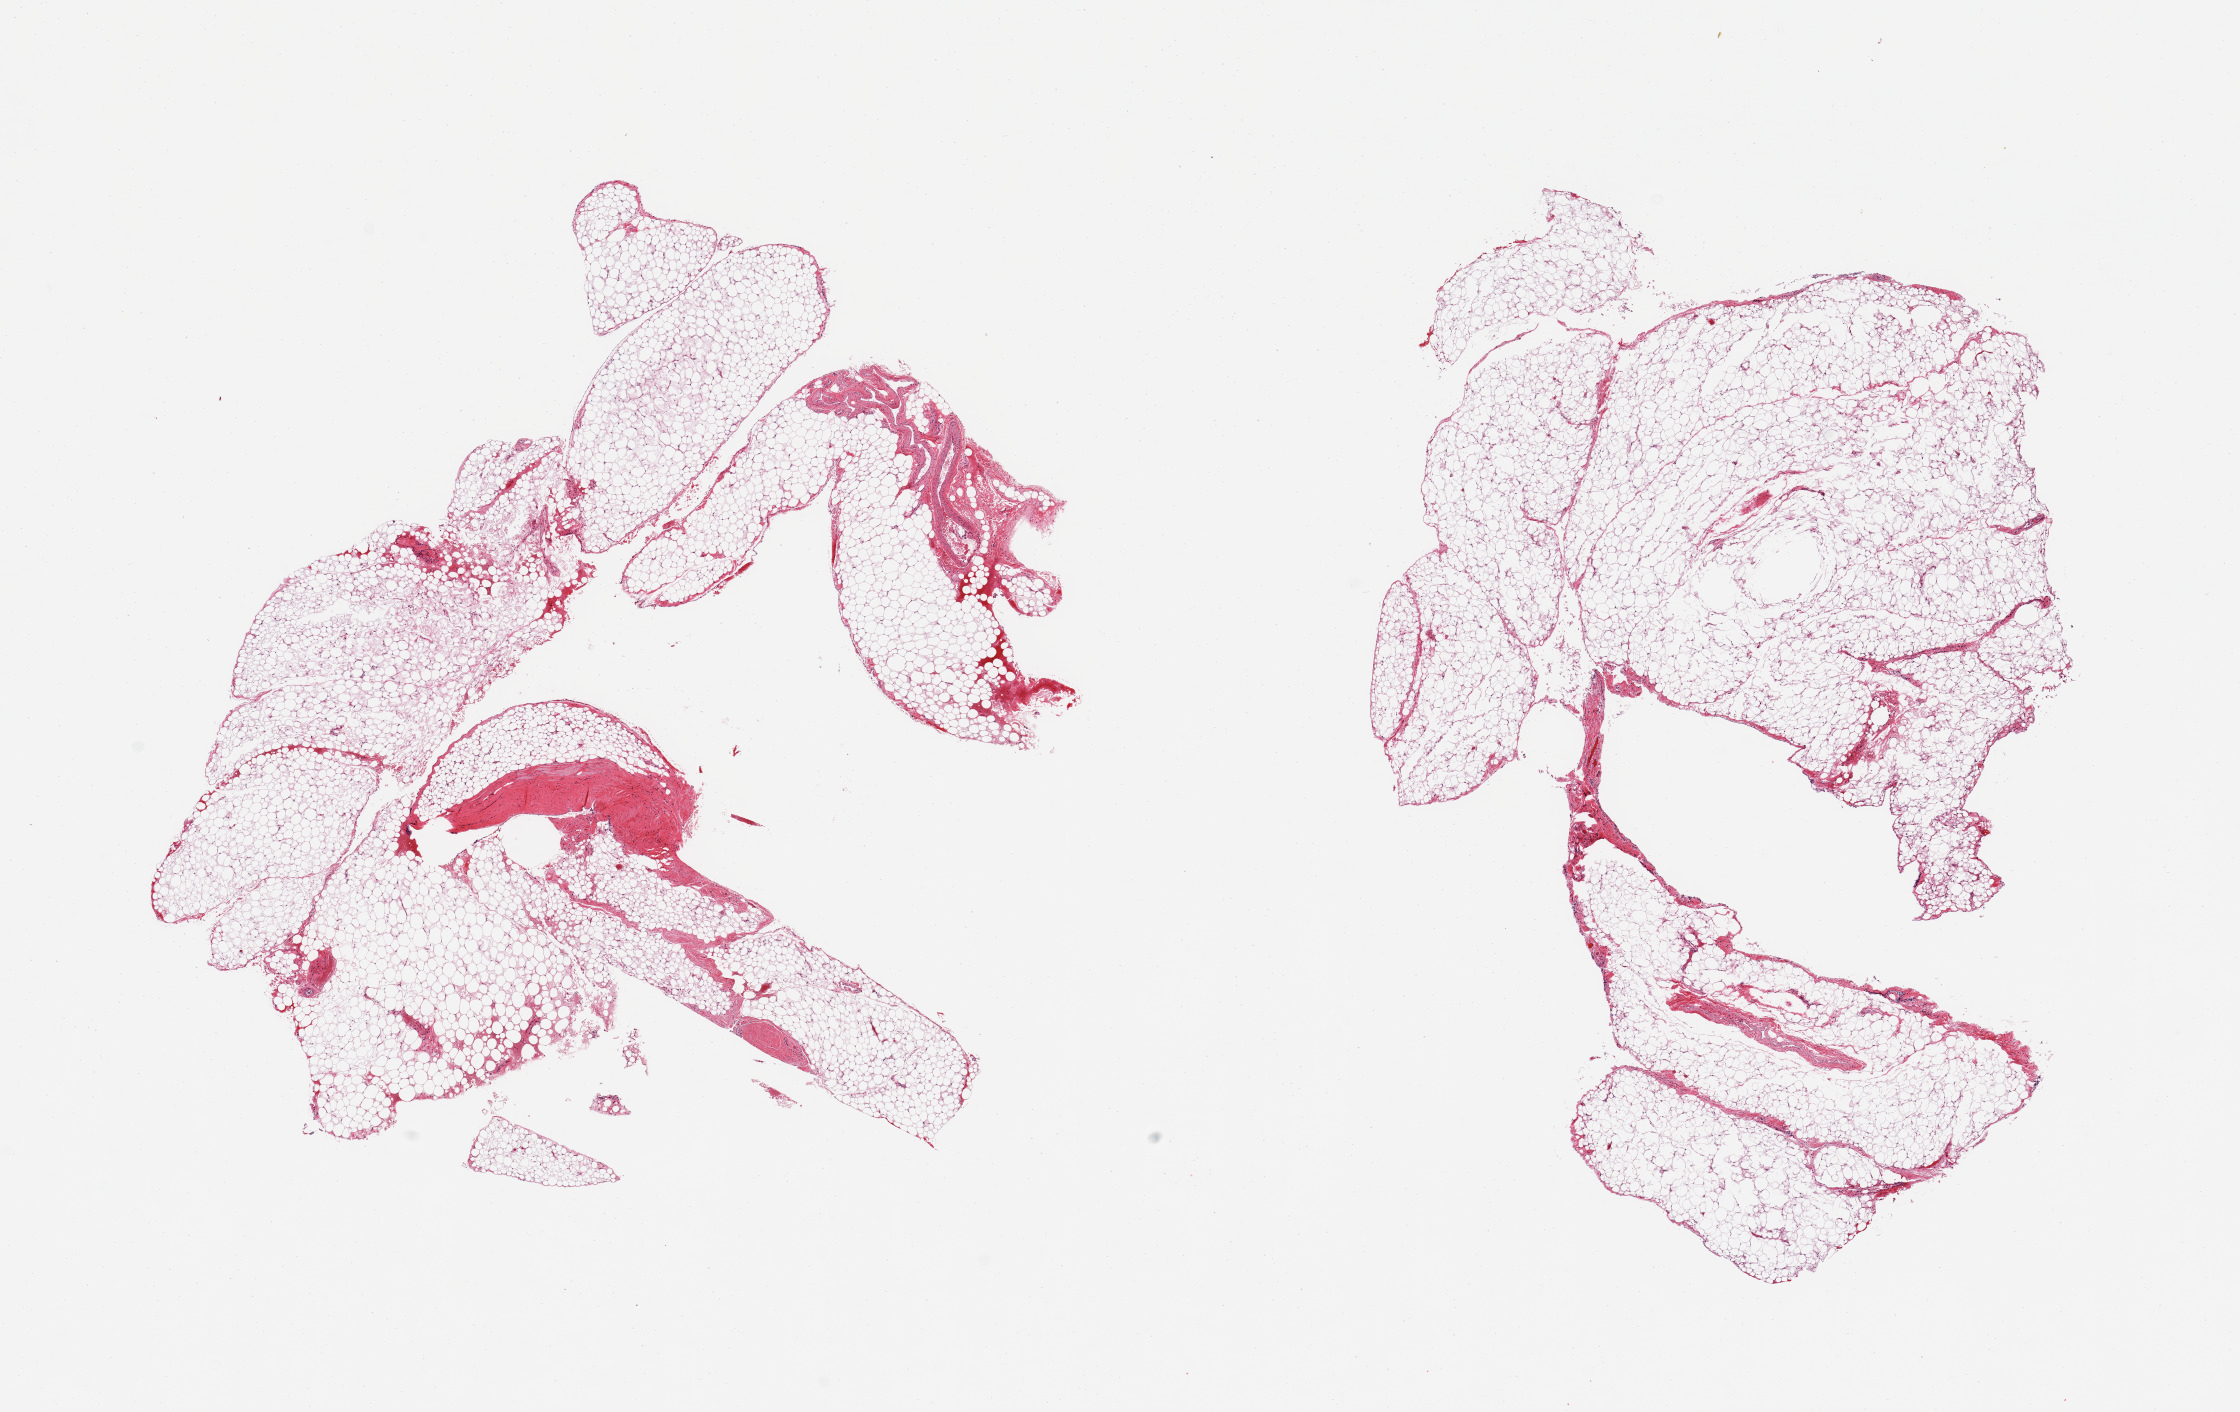
Whole-slide image, H&E stain — shown as a low-resolution overview of the whole scanned area (about 17.7 x 11.2 mm, acquisition: 20x scan); PAXgene-fixed paraffin-embedded (PFPE) section; sampled site (target tissue): omentum; tissue donor sample.
Review note (as recorded): 2 pieces; 5% & 10% fibrovascular tissue content.